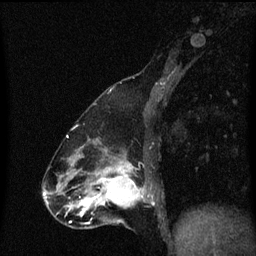
Breast MRI (dynamic contrast-enhanced), one sagittal slice; slice 25 of 60 in the series (ordered by position); dynamic contrast-enhanced series, image 2 of 3 at this slice position (ordered by acquisition); 1.5 T; TE 4.2 ms, TR 8.4 ms; 2 mm slice thickness; 256 × 256 image matrix, field of view 200 × 200 mm. Female patient, age 47 years.
Annotated regions visible in this slice (semi-automatic segmentation, software-assisted and operator-edited):
- analysis volume of interest (the breast-tissue region the enhancement analysis was run in; not a lesion): bounding box <100,172,151,219> (left, top, right, bottom; pixels)
- tumour enhancement mask (voxels above the 70 % enhancement threshold inside the analysis volume of interest): <100,172,145,207>